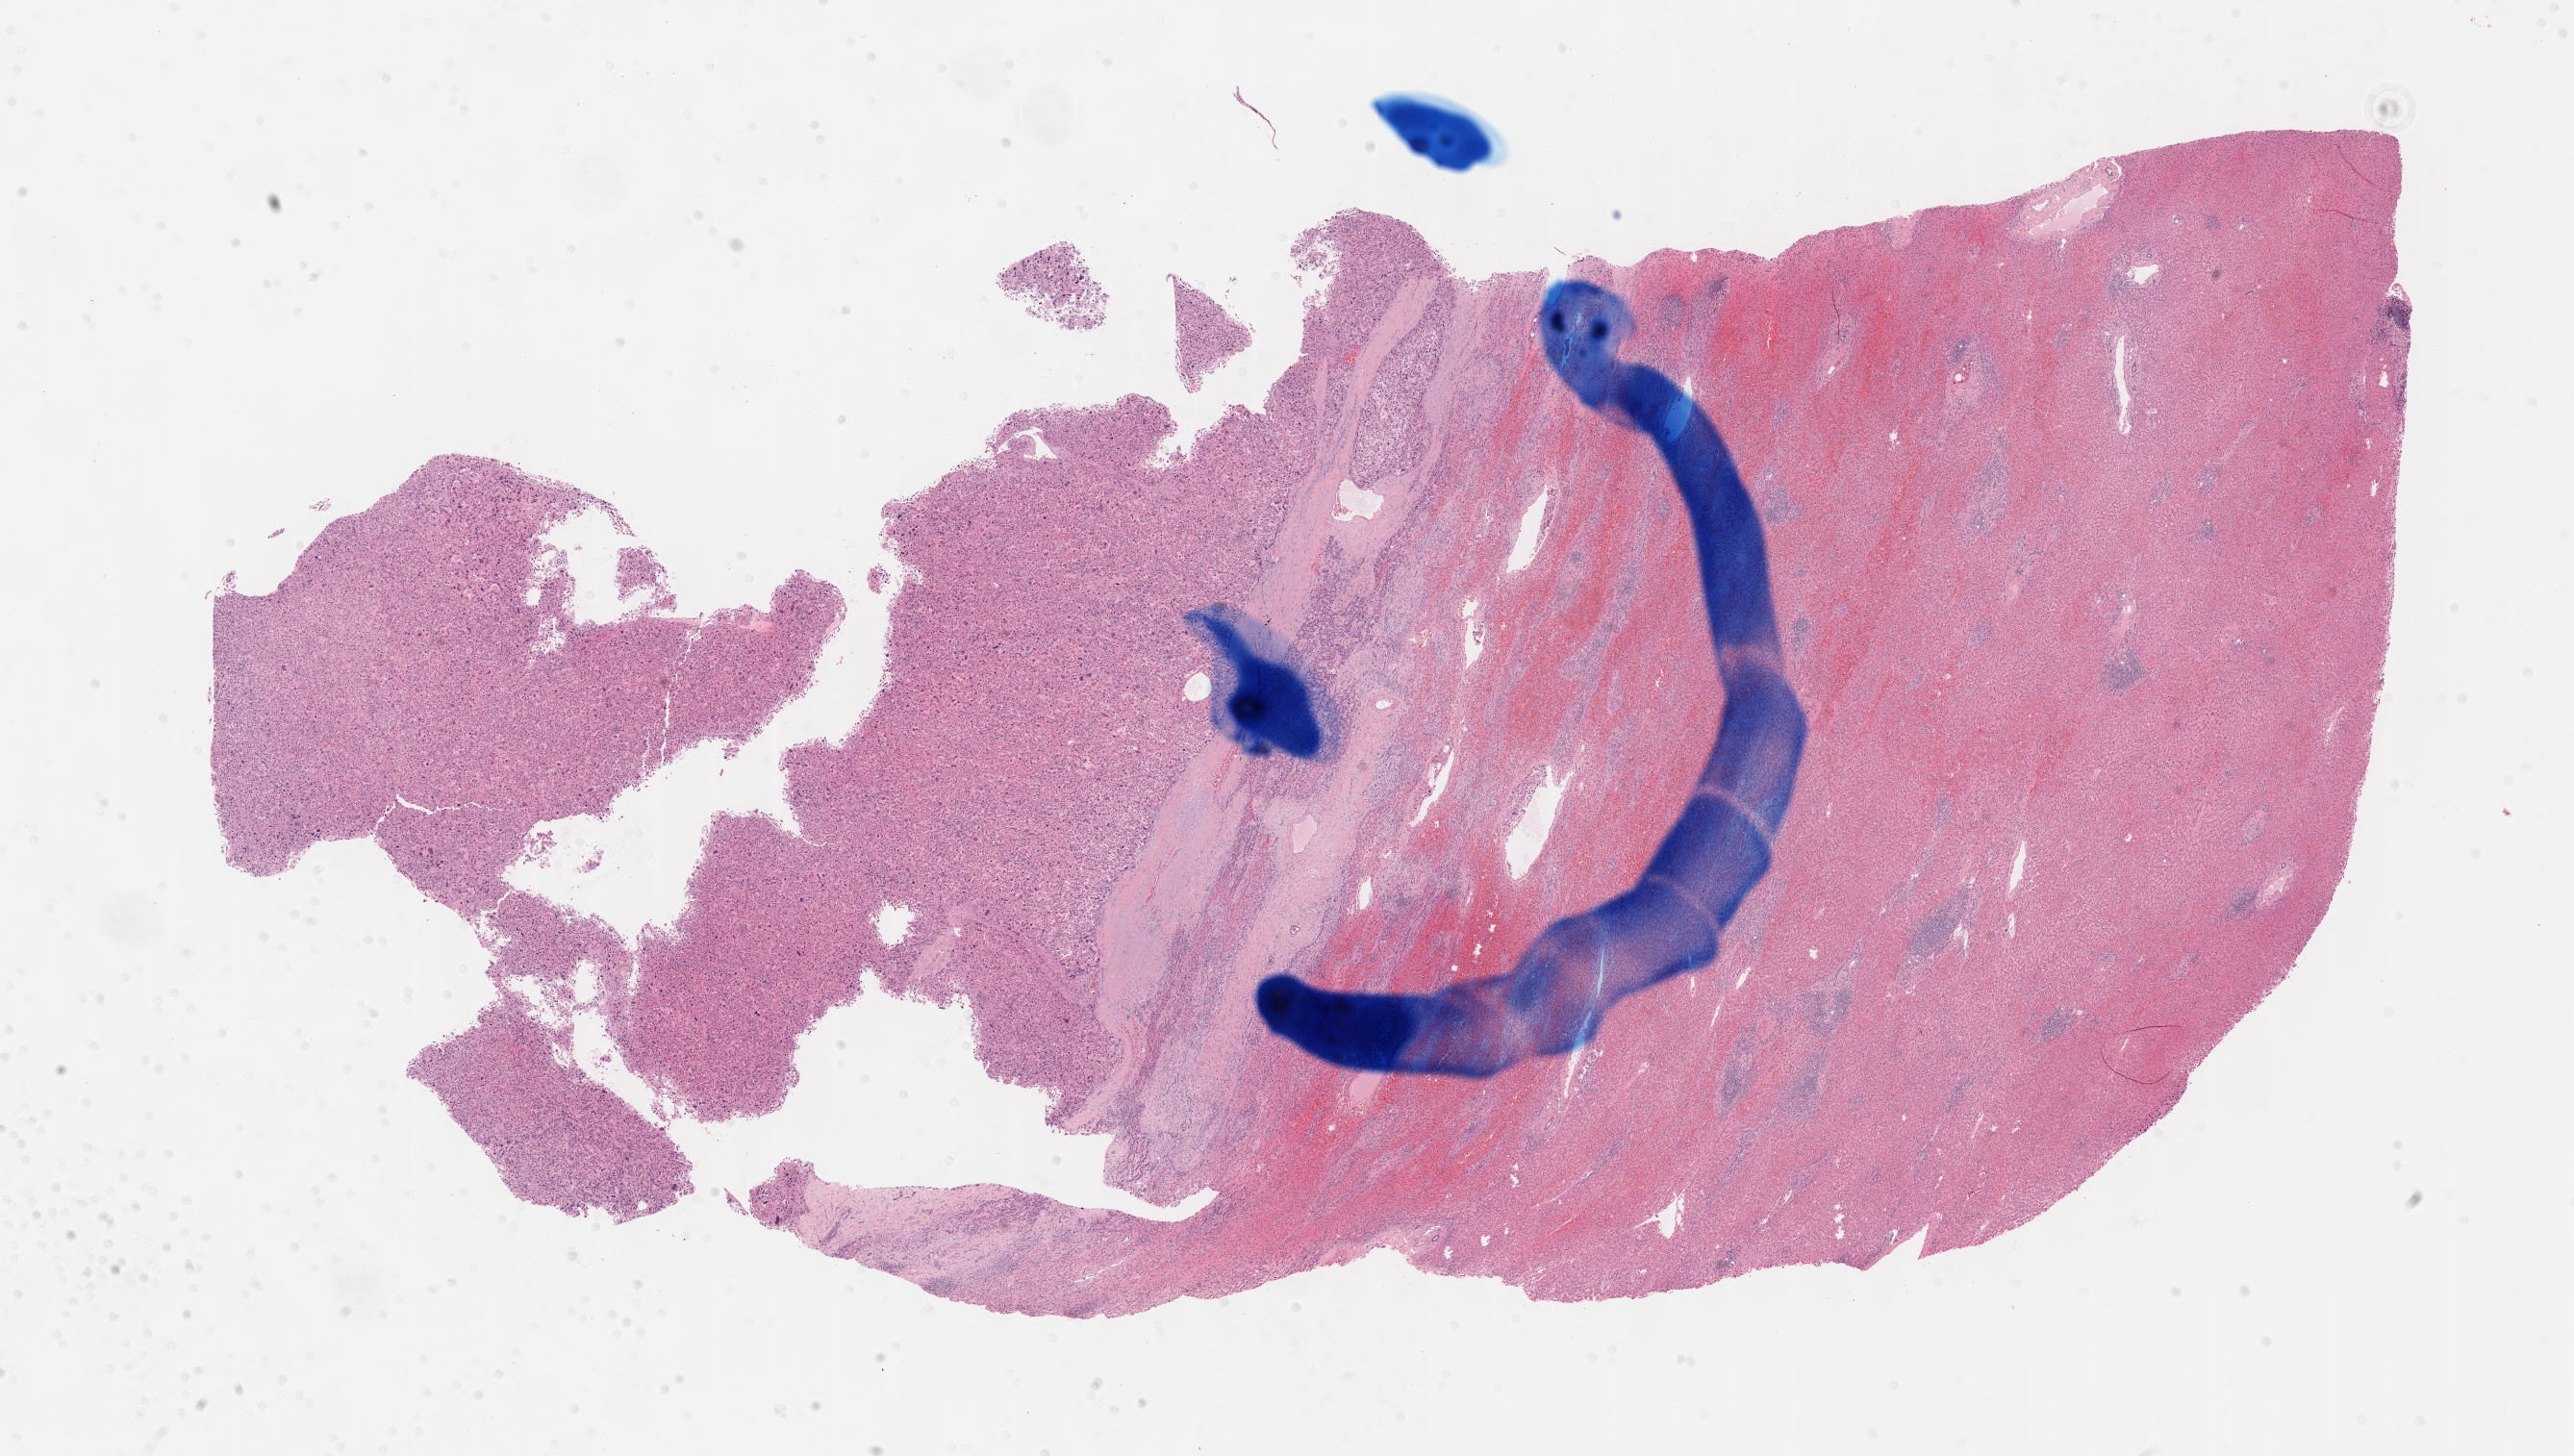
H&E-stained whole-slide image — whole scanned area (about 21.6 x 12.2 mm, from a 40x scan) shown as a low-resolution overview; formalin-fixed paraffin-embedded (FFPE) diagnostic section; sample: primary tumour, liver. Male, age 59 years at initial diagnosis. Histologic grade: G3 (poorly differentiated).
Pathologic diagnosis: Hepatocellular carcinoma, NOS. AJCC pathologic stage: IIIA (7th edition).